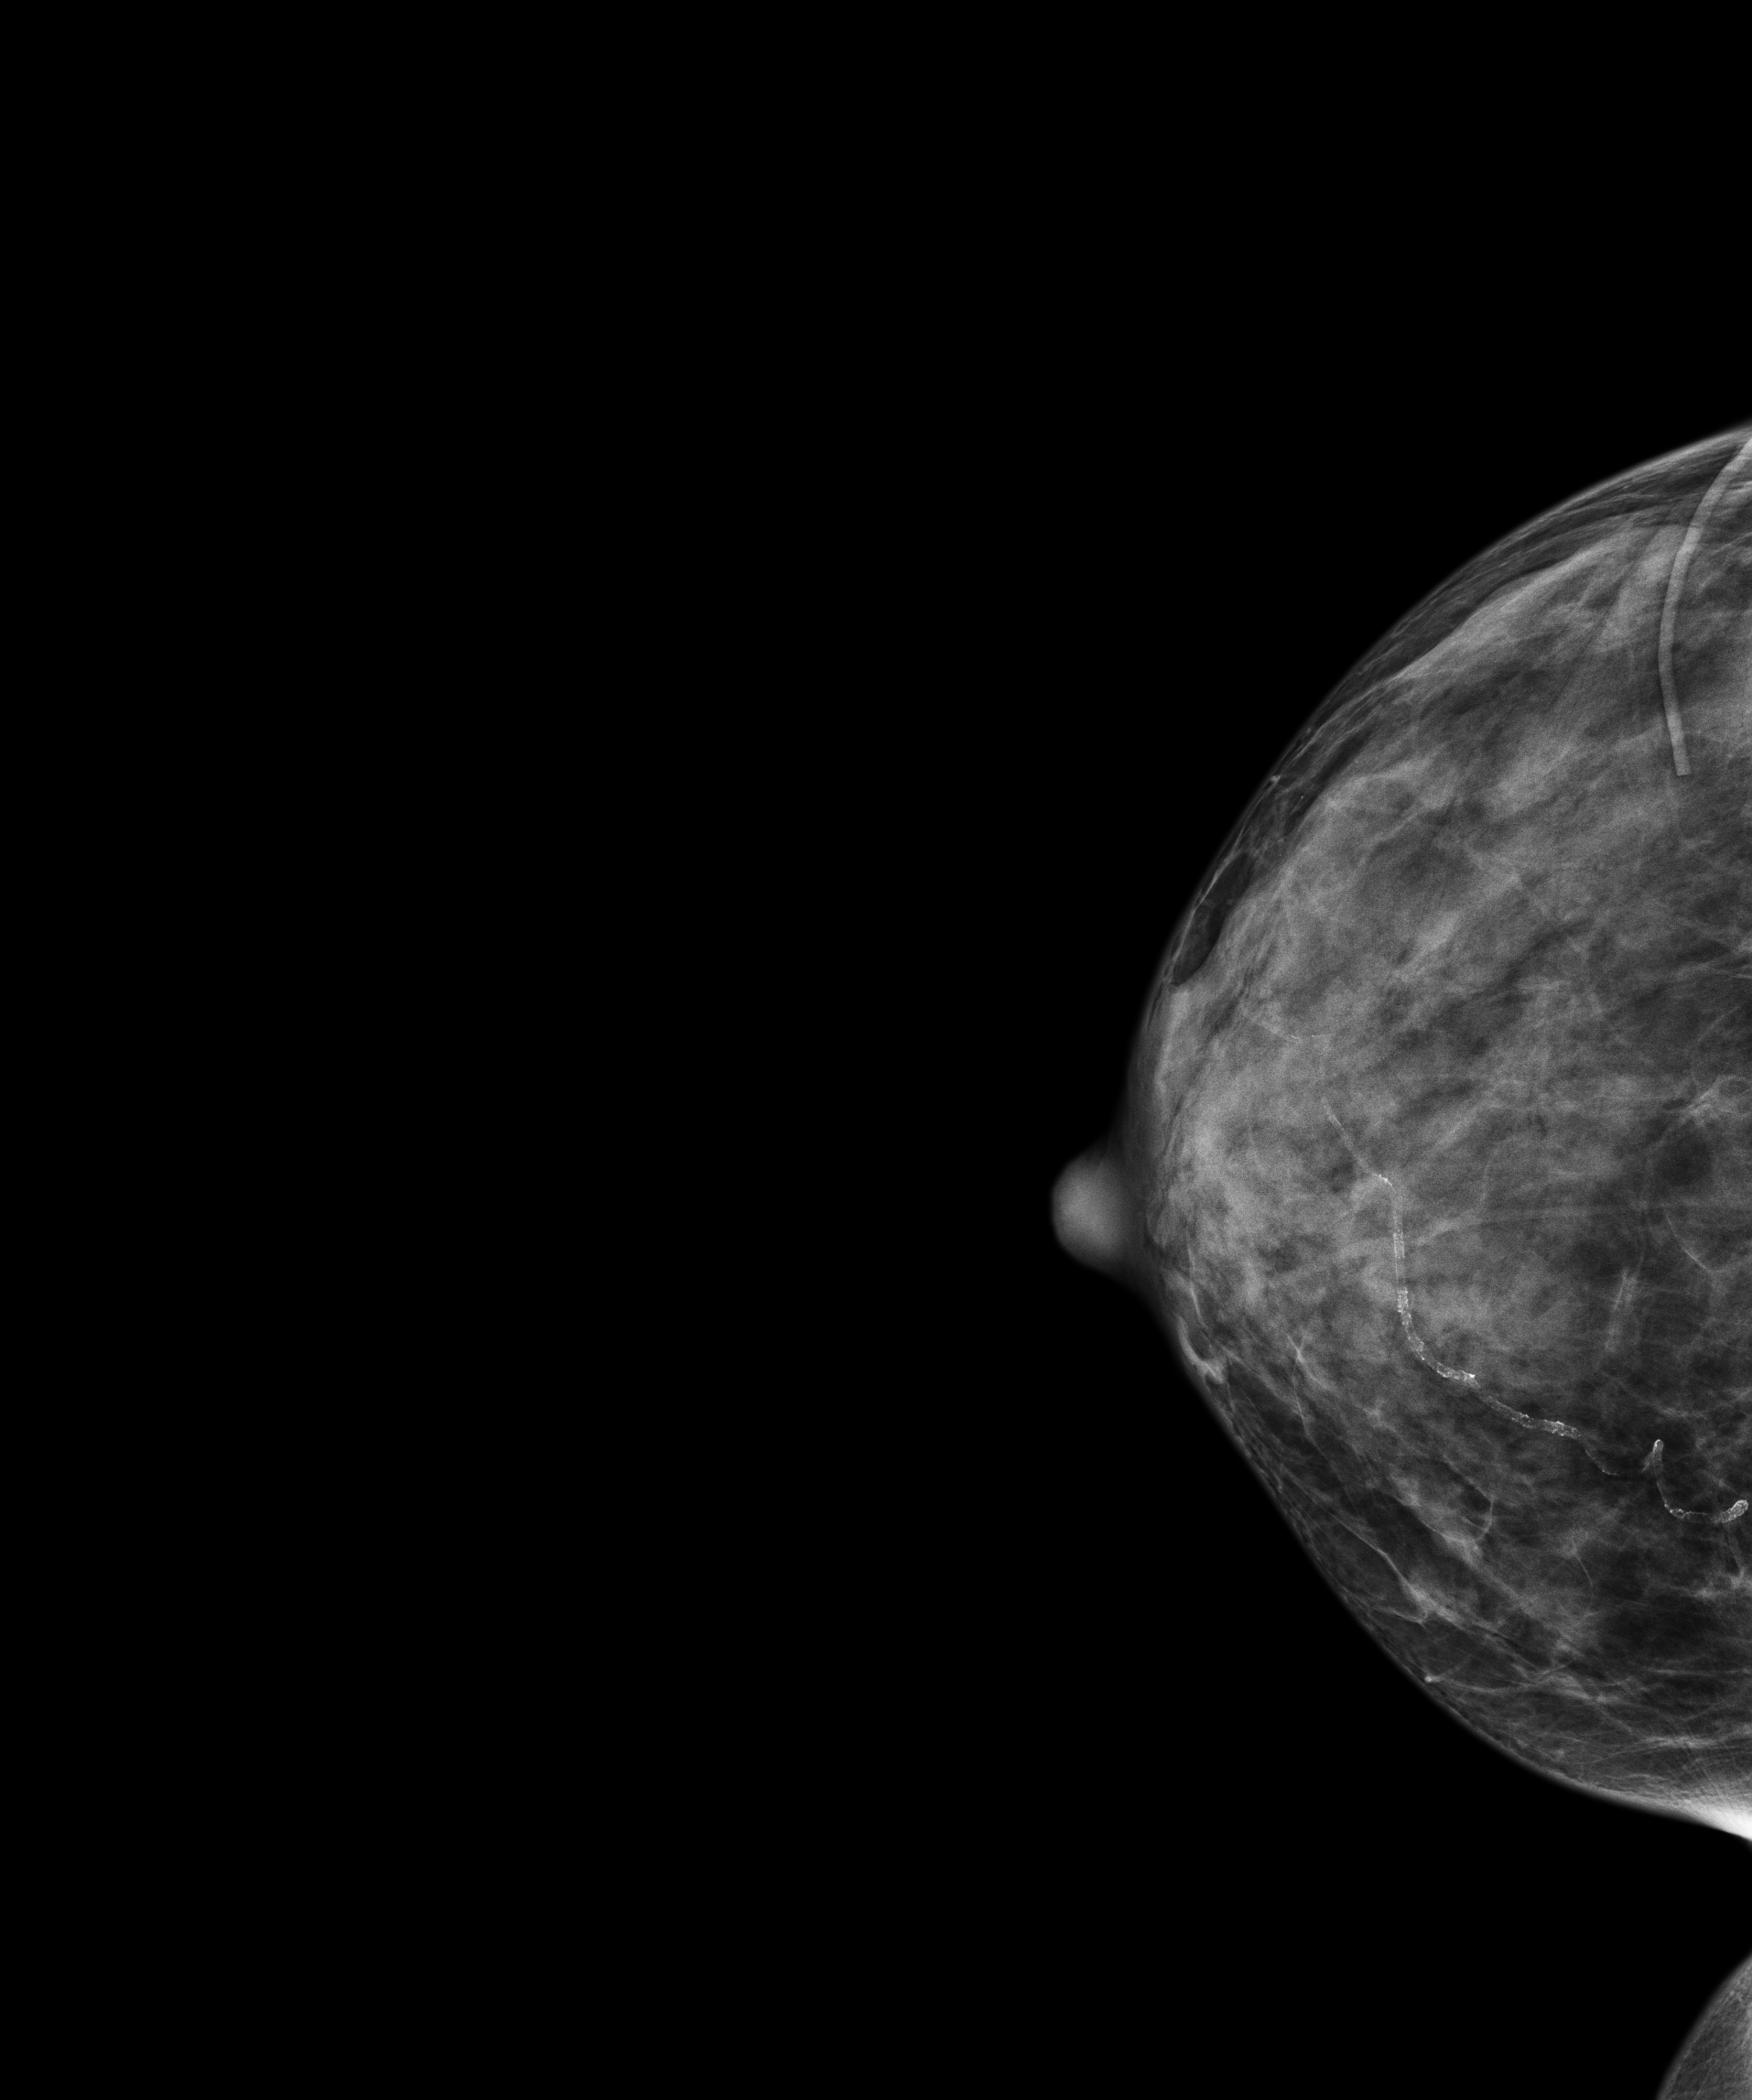
Annual screening mammography examination. Female patient, age 60 years.
Image type: full-field digital mammogram. Breast: right. Projection: cranio-caudal projection.